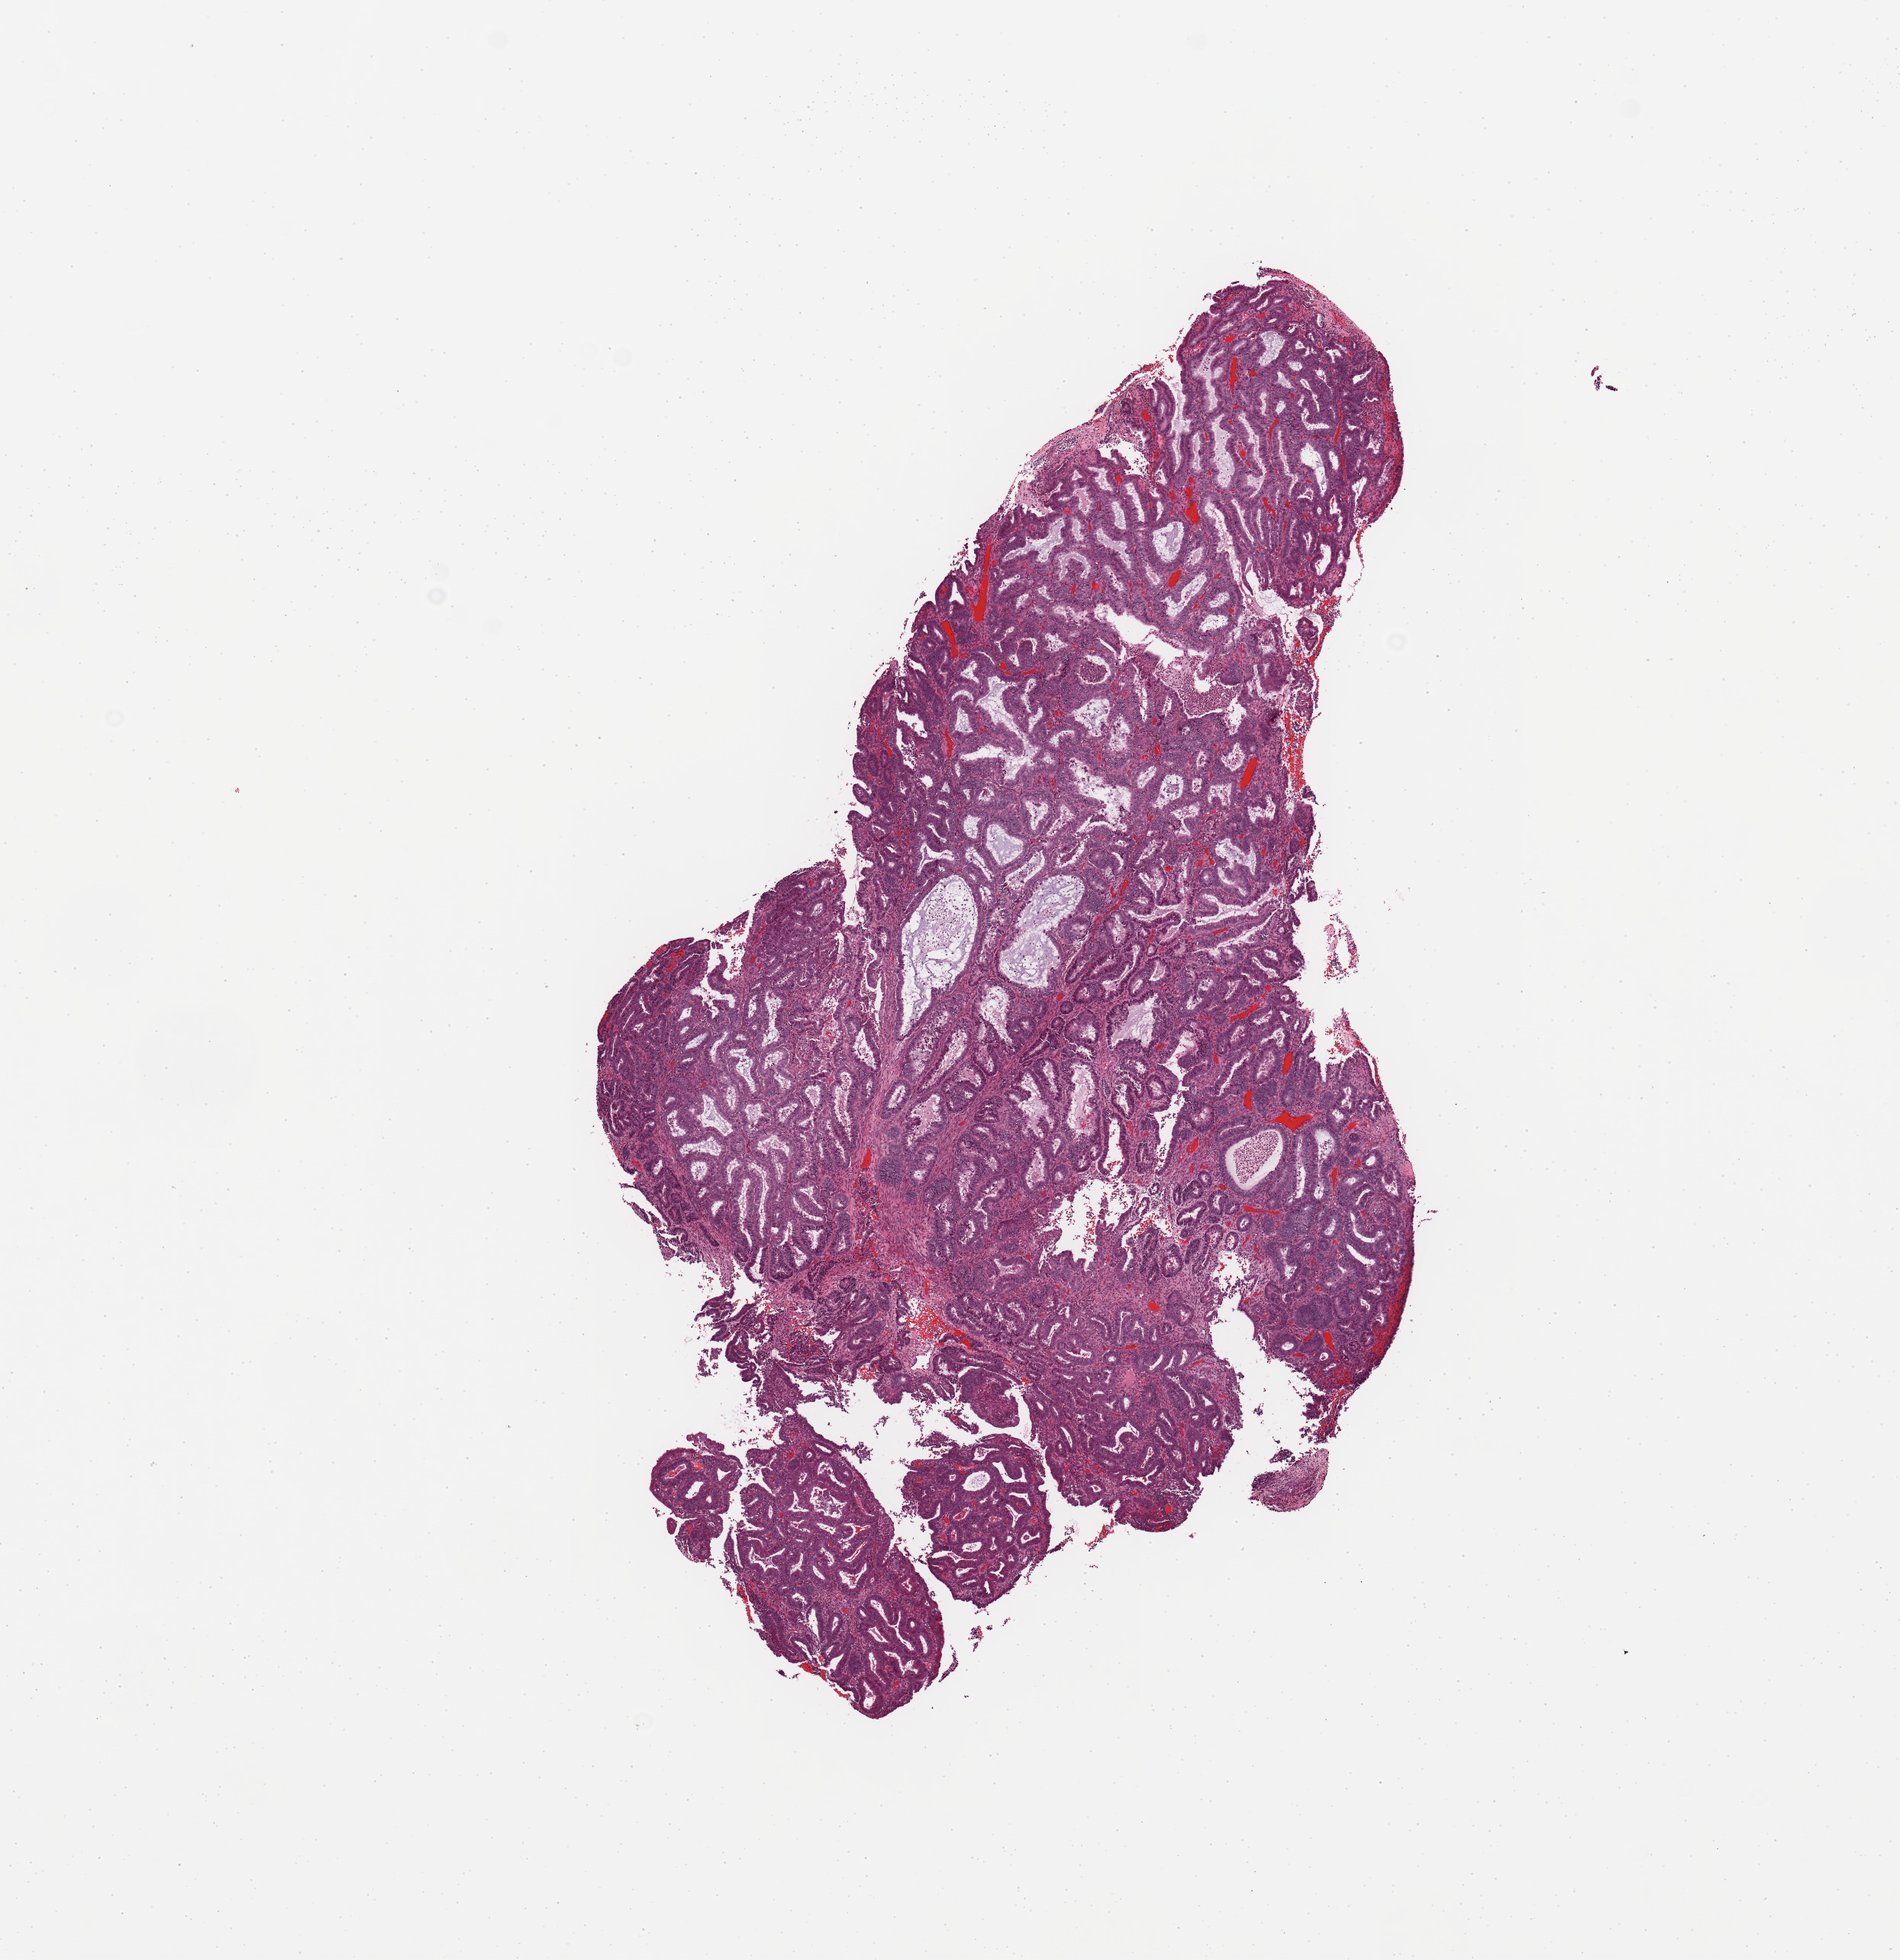
H&E whole-slide image — a low-resolution overview of the entire scanned area, about 9.8 x 10.2 mm (slide scanned at 20x); tumour tissue sample, sampled site: uterus. Female, 56 y/o. Histologic grade: G1 (well differentiated). Slide review estimates, as recorded: tumour nuclei 90%, necrosis 0%.
AJCC pathologic stage: I. Diagnosis: Endometrioid adenocarcinoma, NOS.